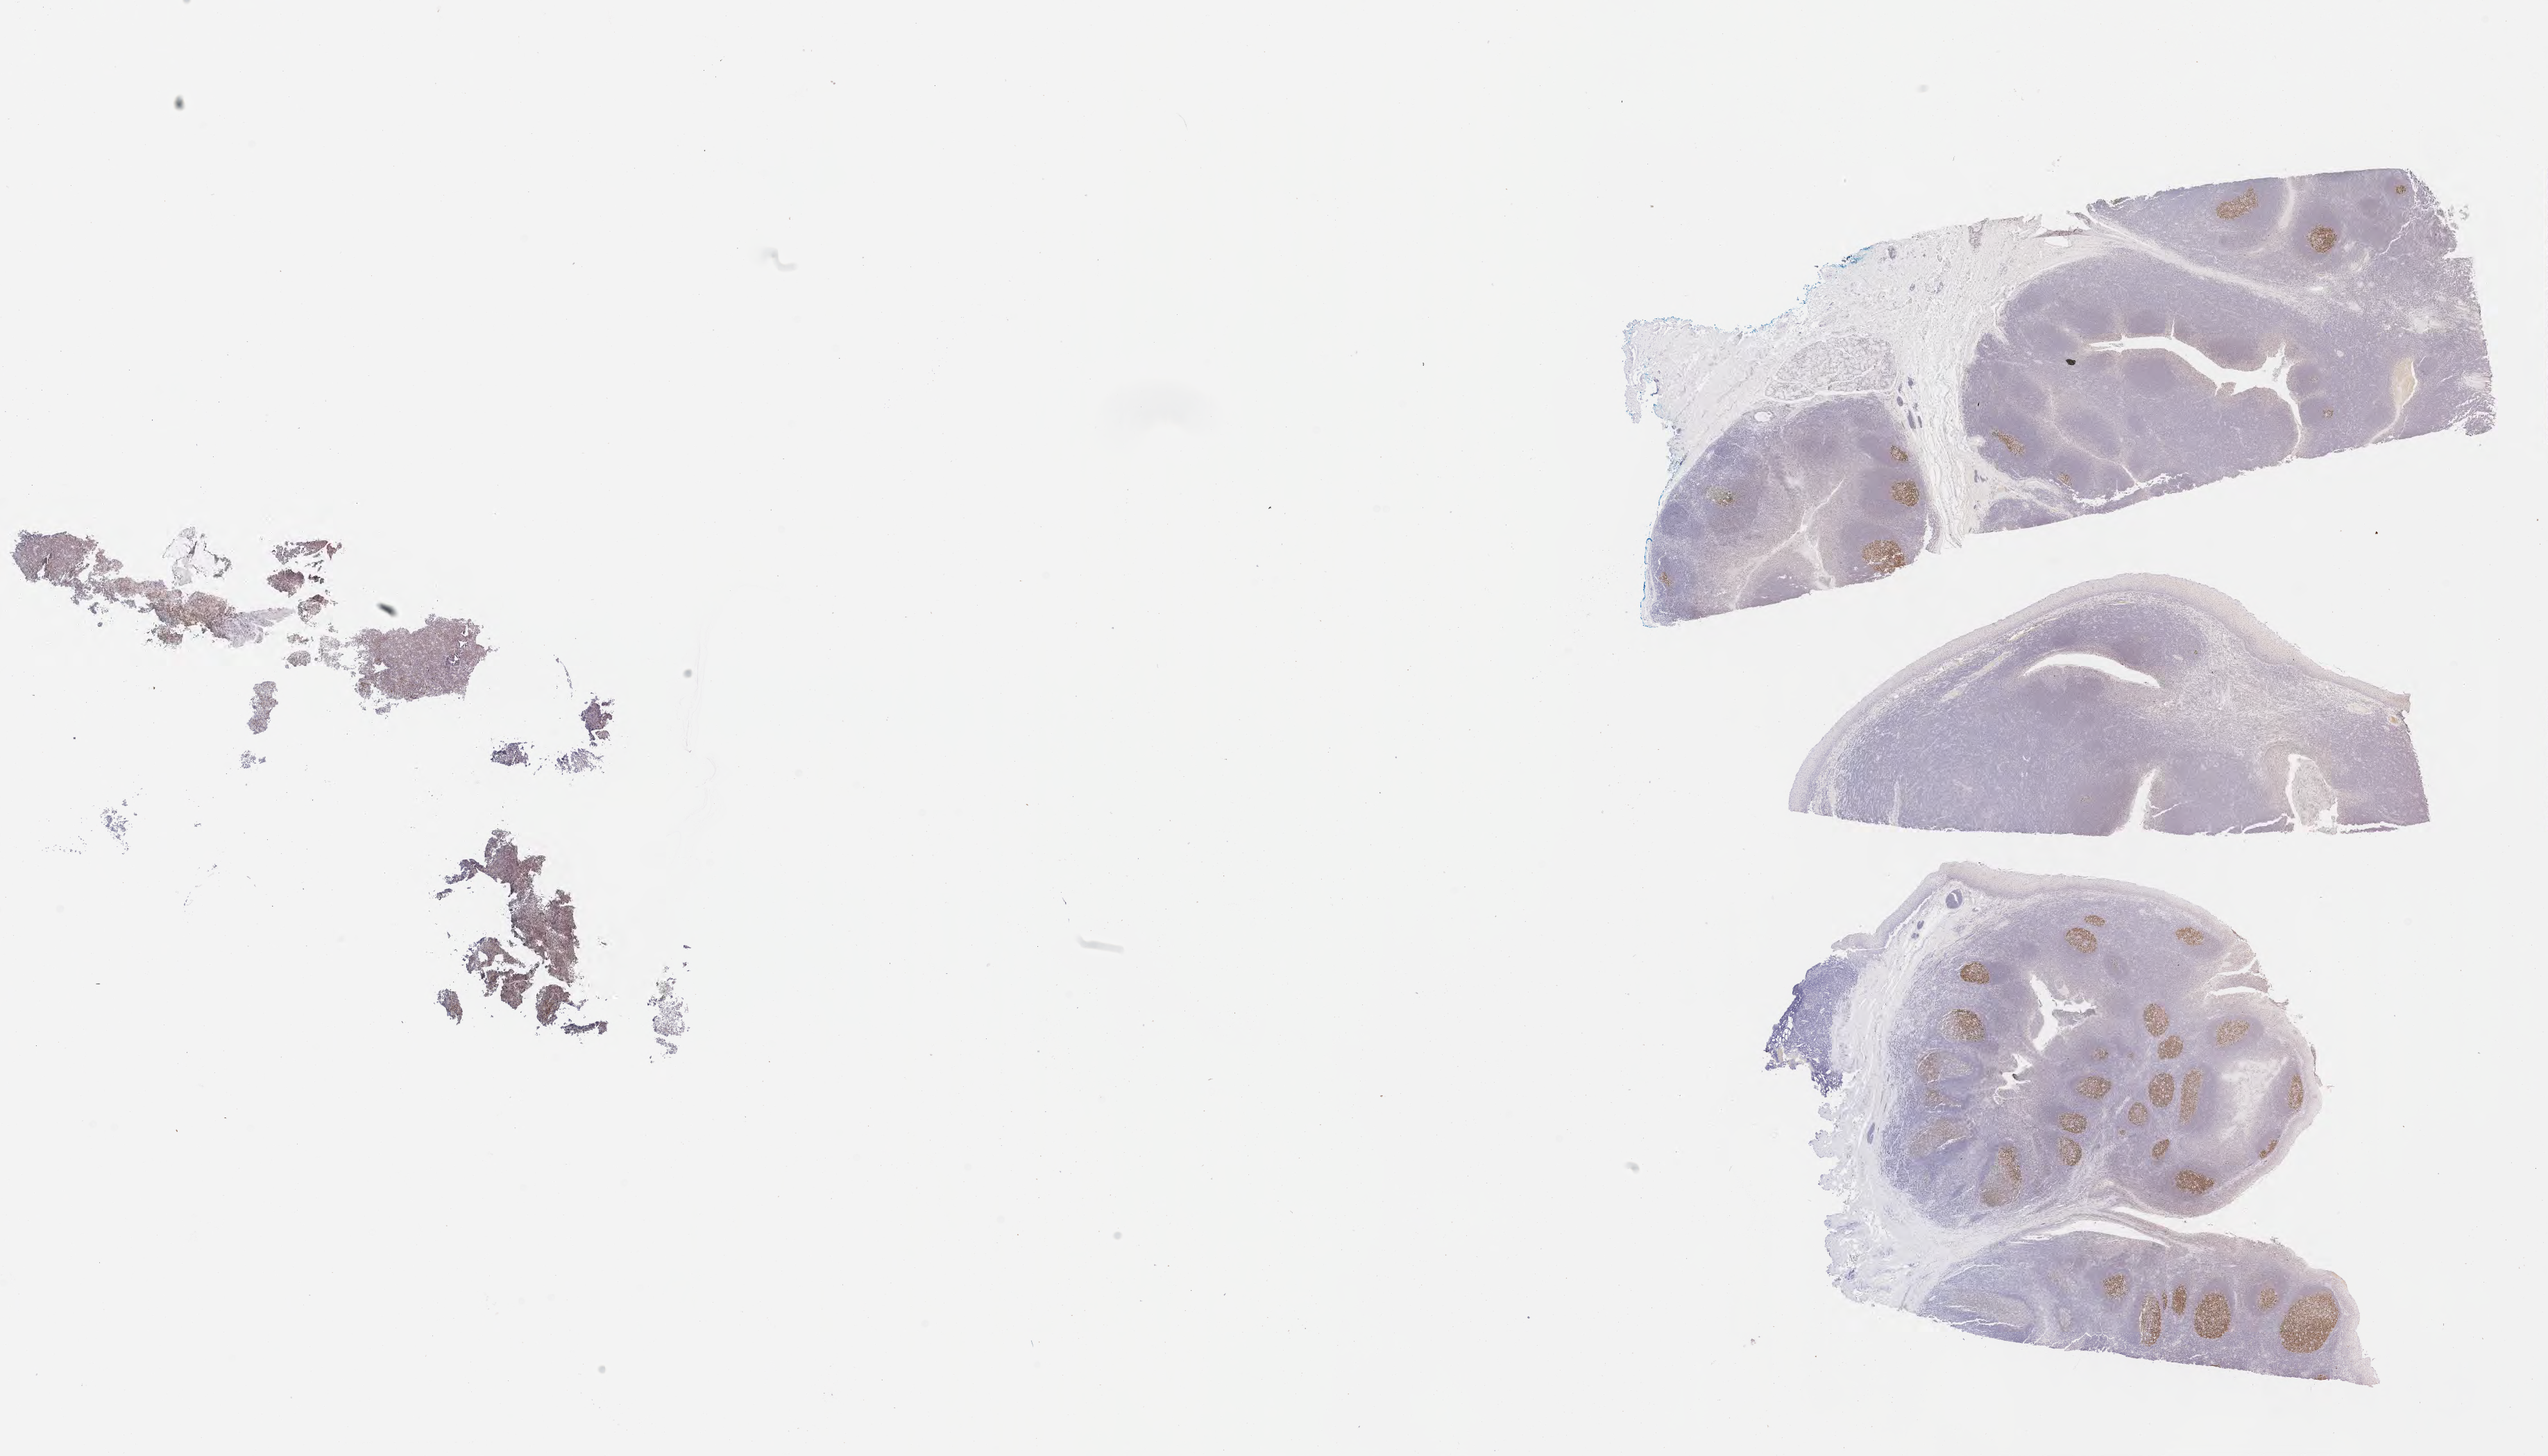
Whole-slide image, immunohistochemical stain for BCL6 — low-resolution overview of the scanned area, about 29.7 x 17.0 mm. Specimen: tumor tissue. Site: cranium. Female patient; age at initial diagnosis 1 years.
Histologic diagnosis: Burkitt lymphoma, NOS.